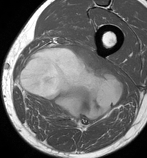
MRI of an extremity soft-tissue mass, one axial slice; position 46 of 86 along the scan axis; MR volume resampled by the dataset authors to the PET/CT grid (not the native acquisition matrix); 147 × 158 image matrix. Male patient. From the clinical record (not read from this slice): histological type: undifferentiated pleomorphic liposarcoma; grade: high; site of the primary tumour: left thigh.
Outlined on this slice (expert contour drawn on MRI and transferred to this co-registered scan by the dataset authors):
- gross tumour volume including surrounding oedema: bounding box (x1, y1, x2, y2) in pixels: (16, 46, 124, 130)
- gross tumour volume (mass): (16, 46, 124, 130)